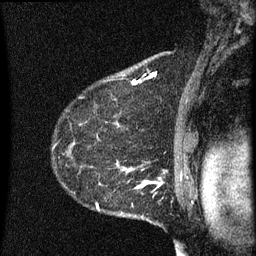
Breast MRI (dynamic contrast-enhanced), one sagittal slice. Position 47 of 60 along the scan axis. Dynamic contrast-enhanced series, image 2 of 3 at this slice position (ordered by acquisition). 1.5 T. TE 4.2 ms, TR 8 ms. 2 mm slice thickness. 256 × 256 image matrix, field of view 180 × 180 mm. Female patient, age 55 years.
Outlined on this slice (semi-automatic segmentation, software-assisted and operator-edited):
- analysis volume of interest (the breast-tissue region the enhancement analysis was run in; not a lesion): bounding box [x1, y1, x2, y2] px = [51, 156, 145, 217]
- tumour enhancement mask (voxels above the 70 % enhancement threshold inside the analysis volume of interest): [97, 170, 145, 211]